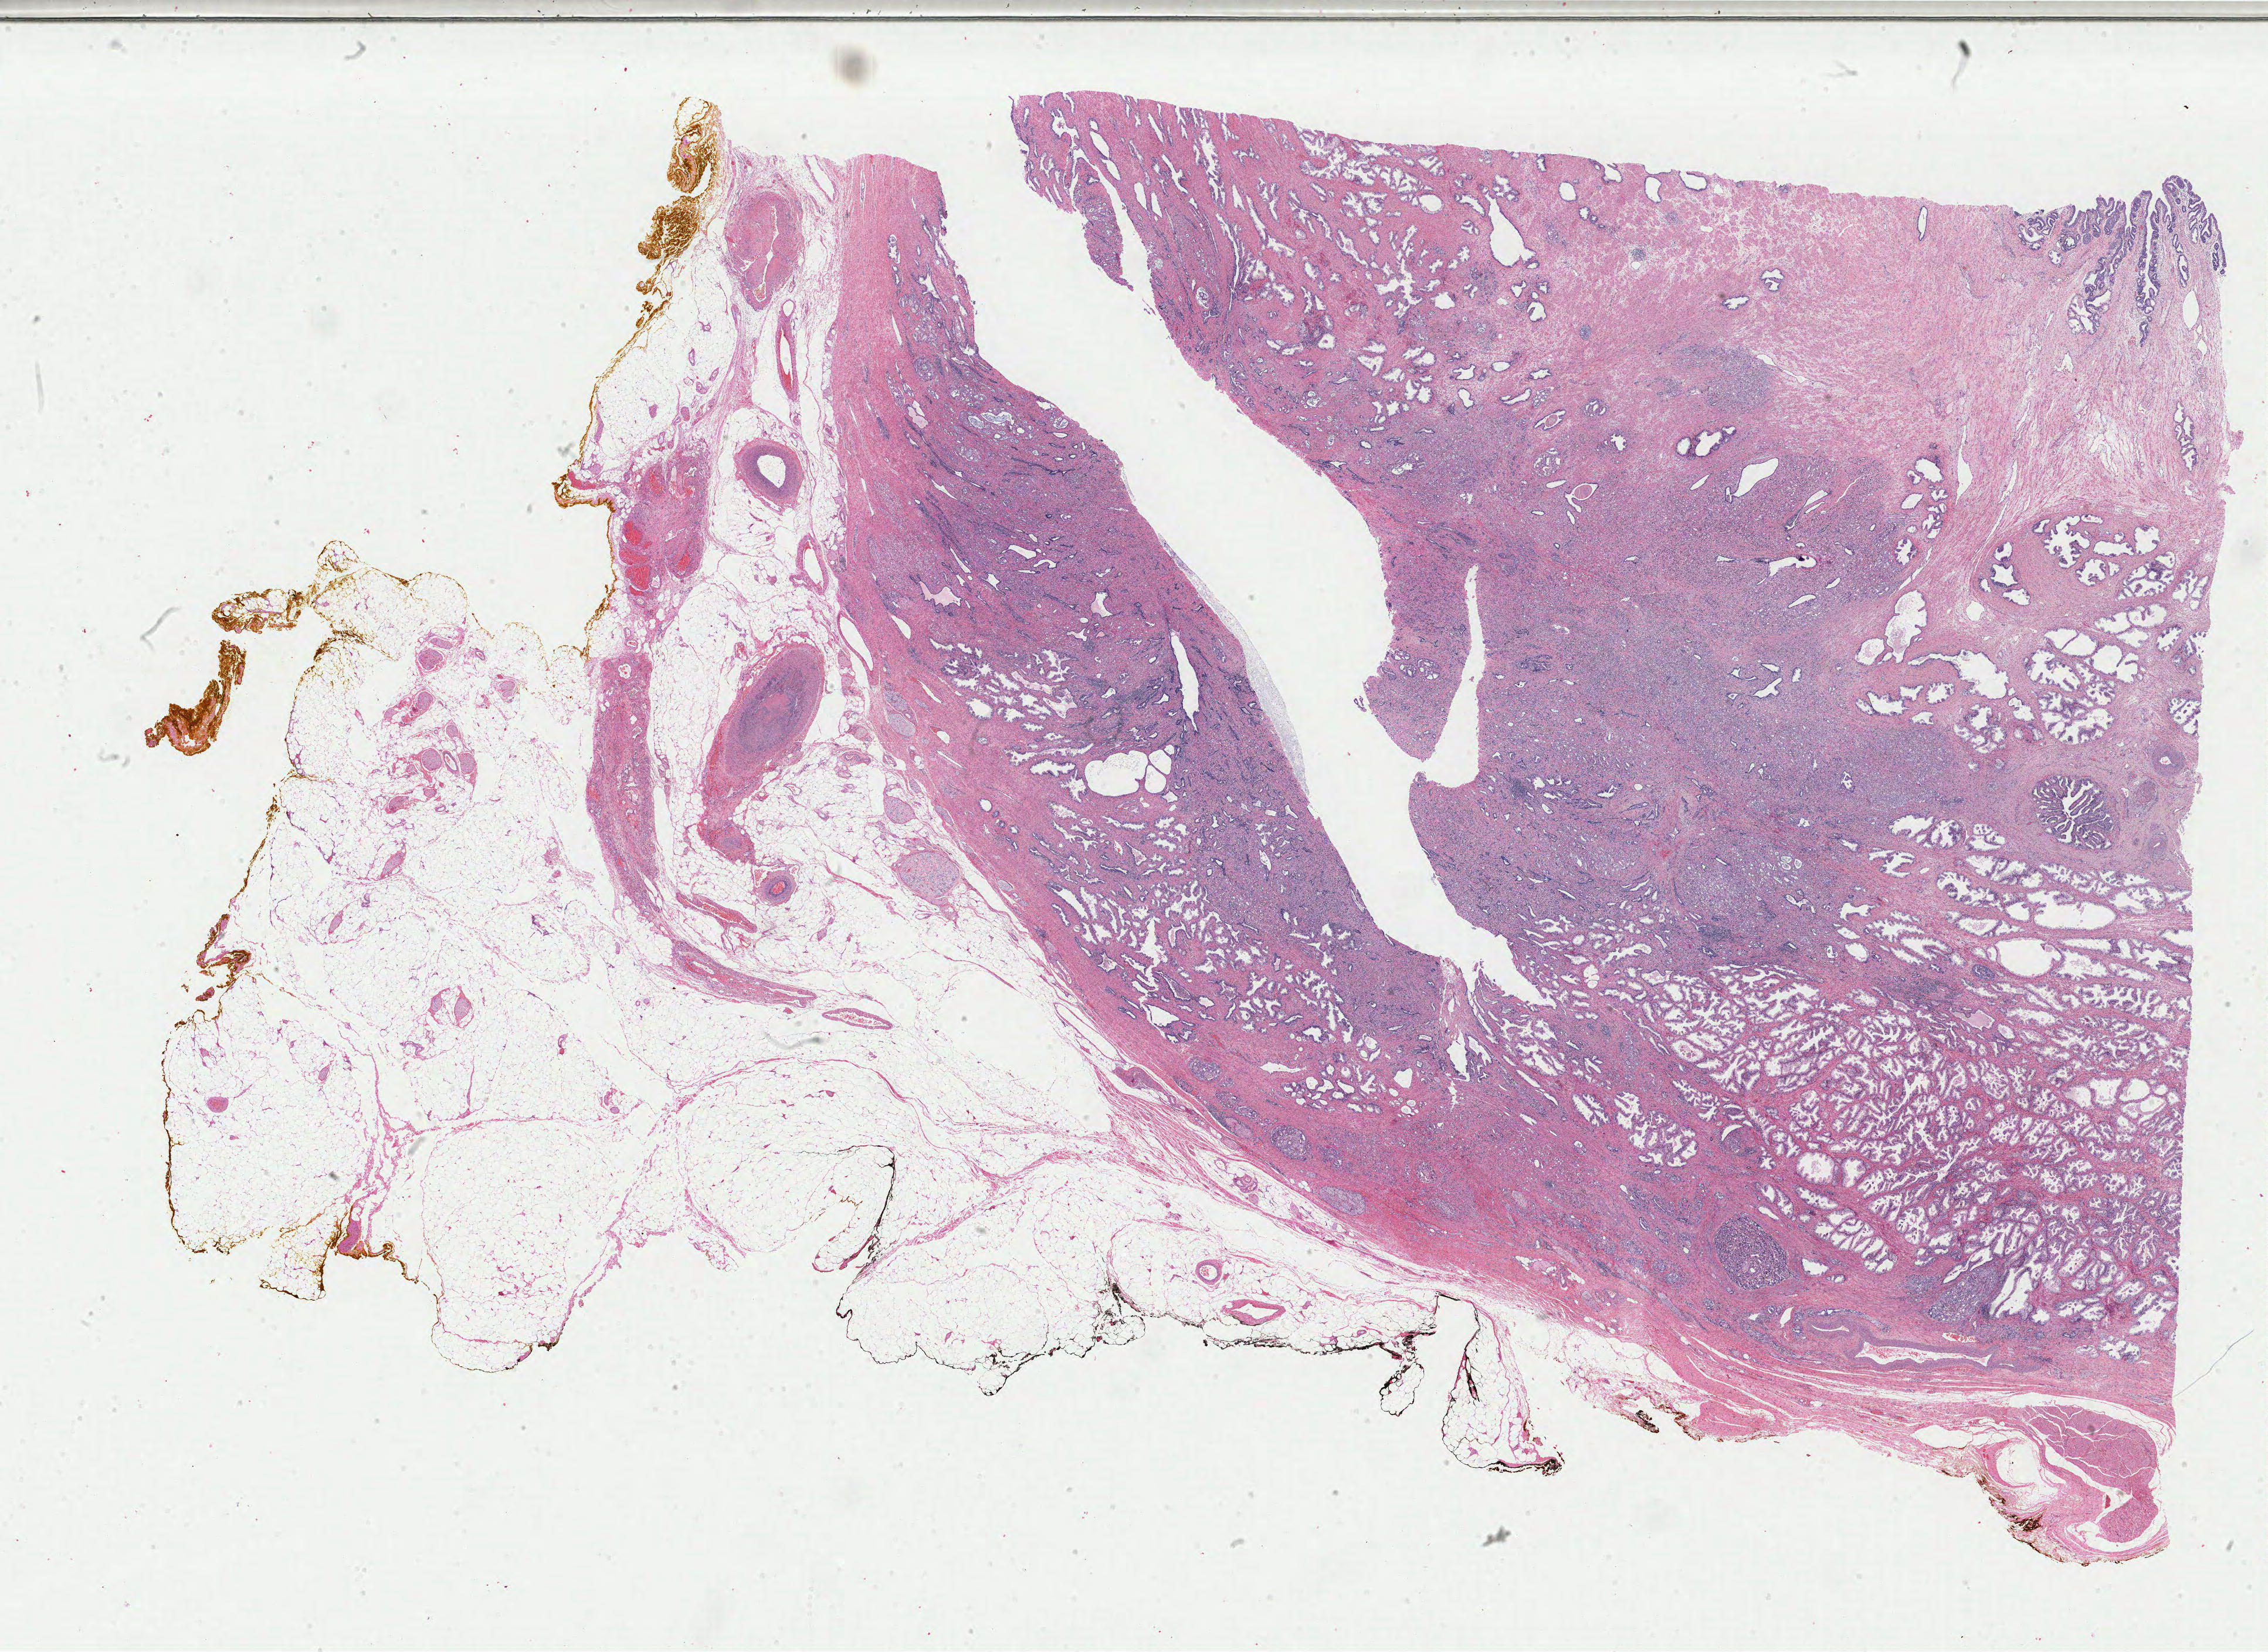
H&E whole-slide image, shown as a low-resolution overview of the whole scanned area (about 30.7 x 22.4 mm, from a 40x scan), FFPE section, primary tumour sample from the prostate. Male, age 54 years at initial diagnosis. Gleason score: 9 (4+5).
Histologic diagnosis: Adenocarcinoma, NOS (prostate gland).